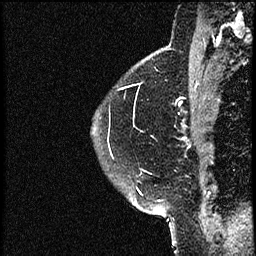
Breast MRI (dynamic contrast-enhanced), one sagittal slice; slice 45 of 52 in the series (ordered by position); dynamic contrast-enhanced study with each time point stored as its own series, time point 2 of 3 at this slice position (early post-contrast, ordered by acquisition time); 1.5 T; TE 4.2 ms, TR 17.6 ms; 2 mm slice thickness; 256 × 256 image matrix, field of view 200 × 200 mm. Patient: female, 49 years. Case-level facts recorded for this patient, not image findings: setting: breast cancer imaged before/during neoadjuvant chemotherapy; receptor status: HER2-positive.
Annotated regions visible in this slice (semi-automatic segmentation, software-assisted and operator-edited):
- analysis volume of interest (the breast-tissue region the enhancement analysis was run in; not a lesion): bounding box [x1, y1, x2, y2] px = [92, 65, 182, 175]
- tumour enhancement mask (voxels above the 100 % enhancement threshold inside the analysis volume of interest): [121, 88, 182, 105]